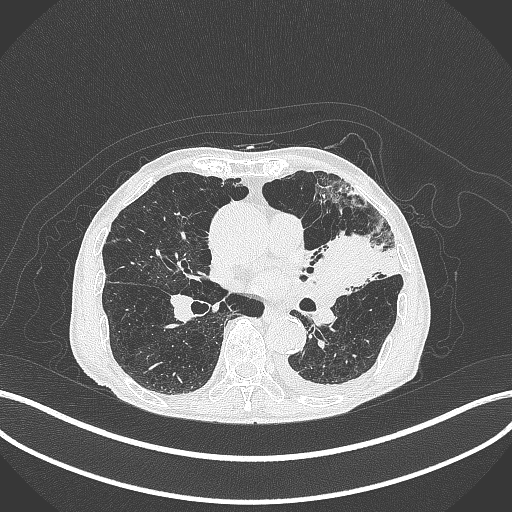
Chest CT, one axial slice. Slice 192 of 385 in the series (ordered by position). Reconstruction kernel B70f. 120 kVp. Lung window (W 1500 / L -600 HU). 512 × 512 image matrix, field of view 400 × 400 mm. Patient: male, 90 years or older. From the clinical record (not read from this slice): clinical TNM (as recorded): T2b N1 M0.
Annotated regions visible in this slice (rectangle marked by the reading radiologist):
- lung tumour (recorded histology: squamous cell carcinoma): bounding box <314,227,380,295> (left, top, right, bottom; pixels)